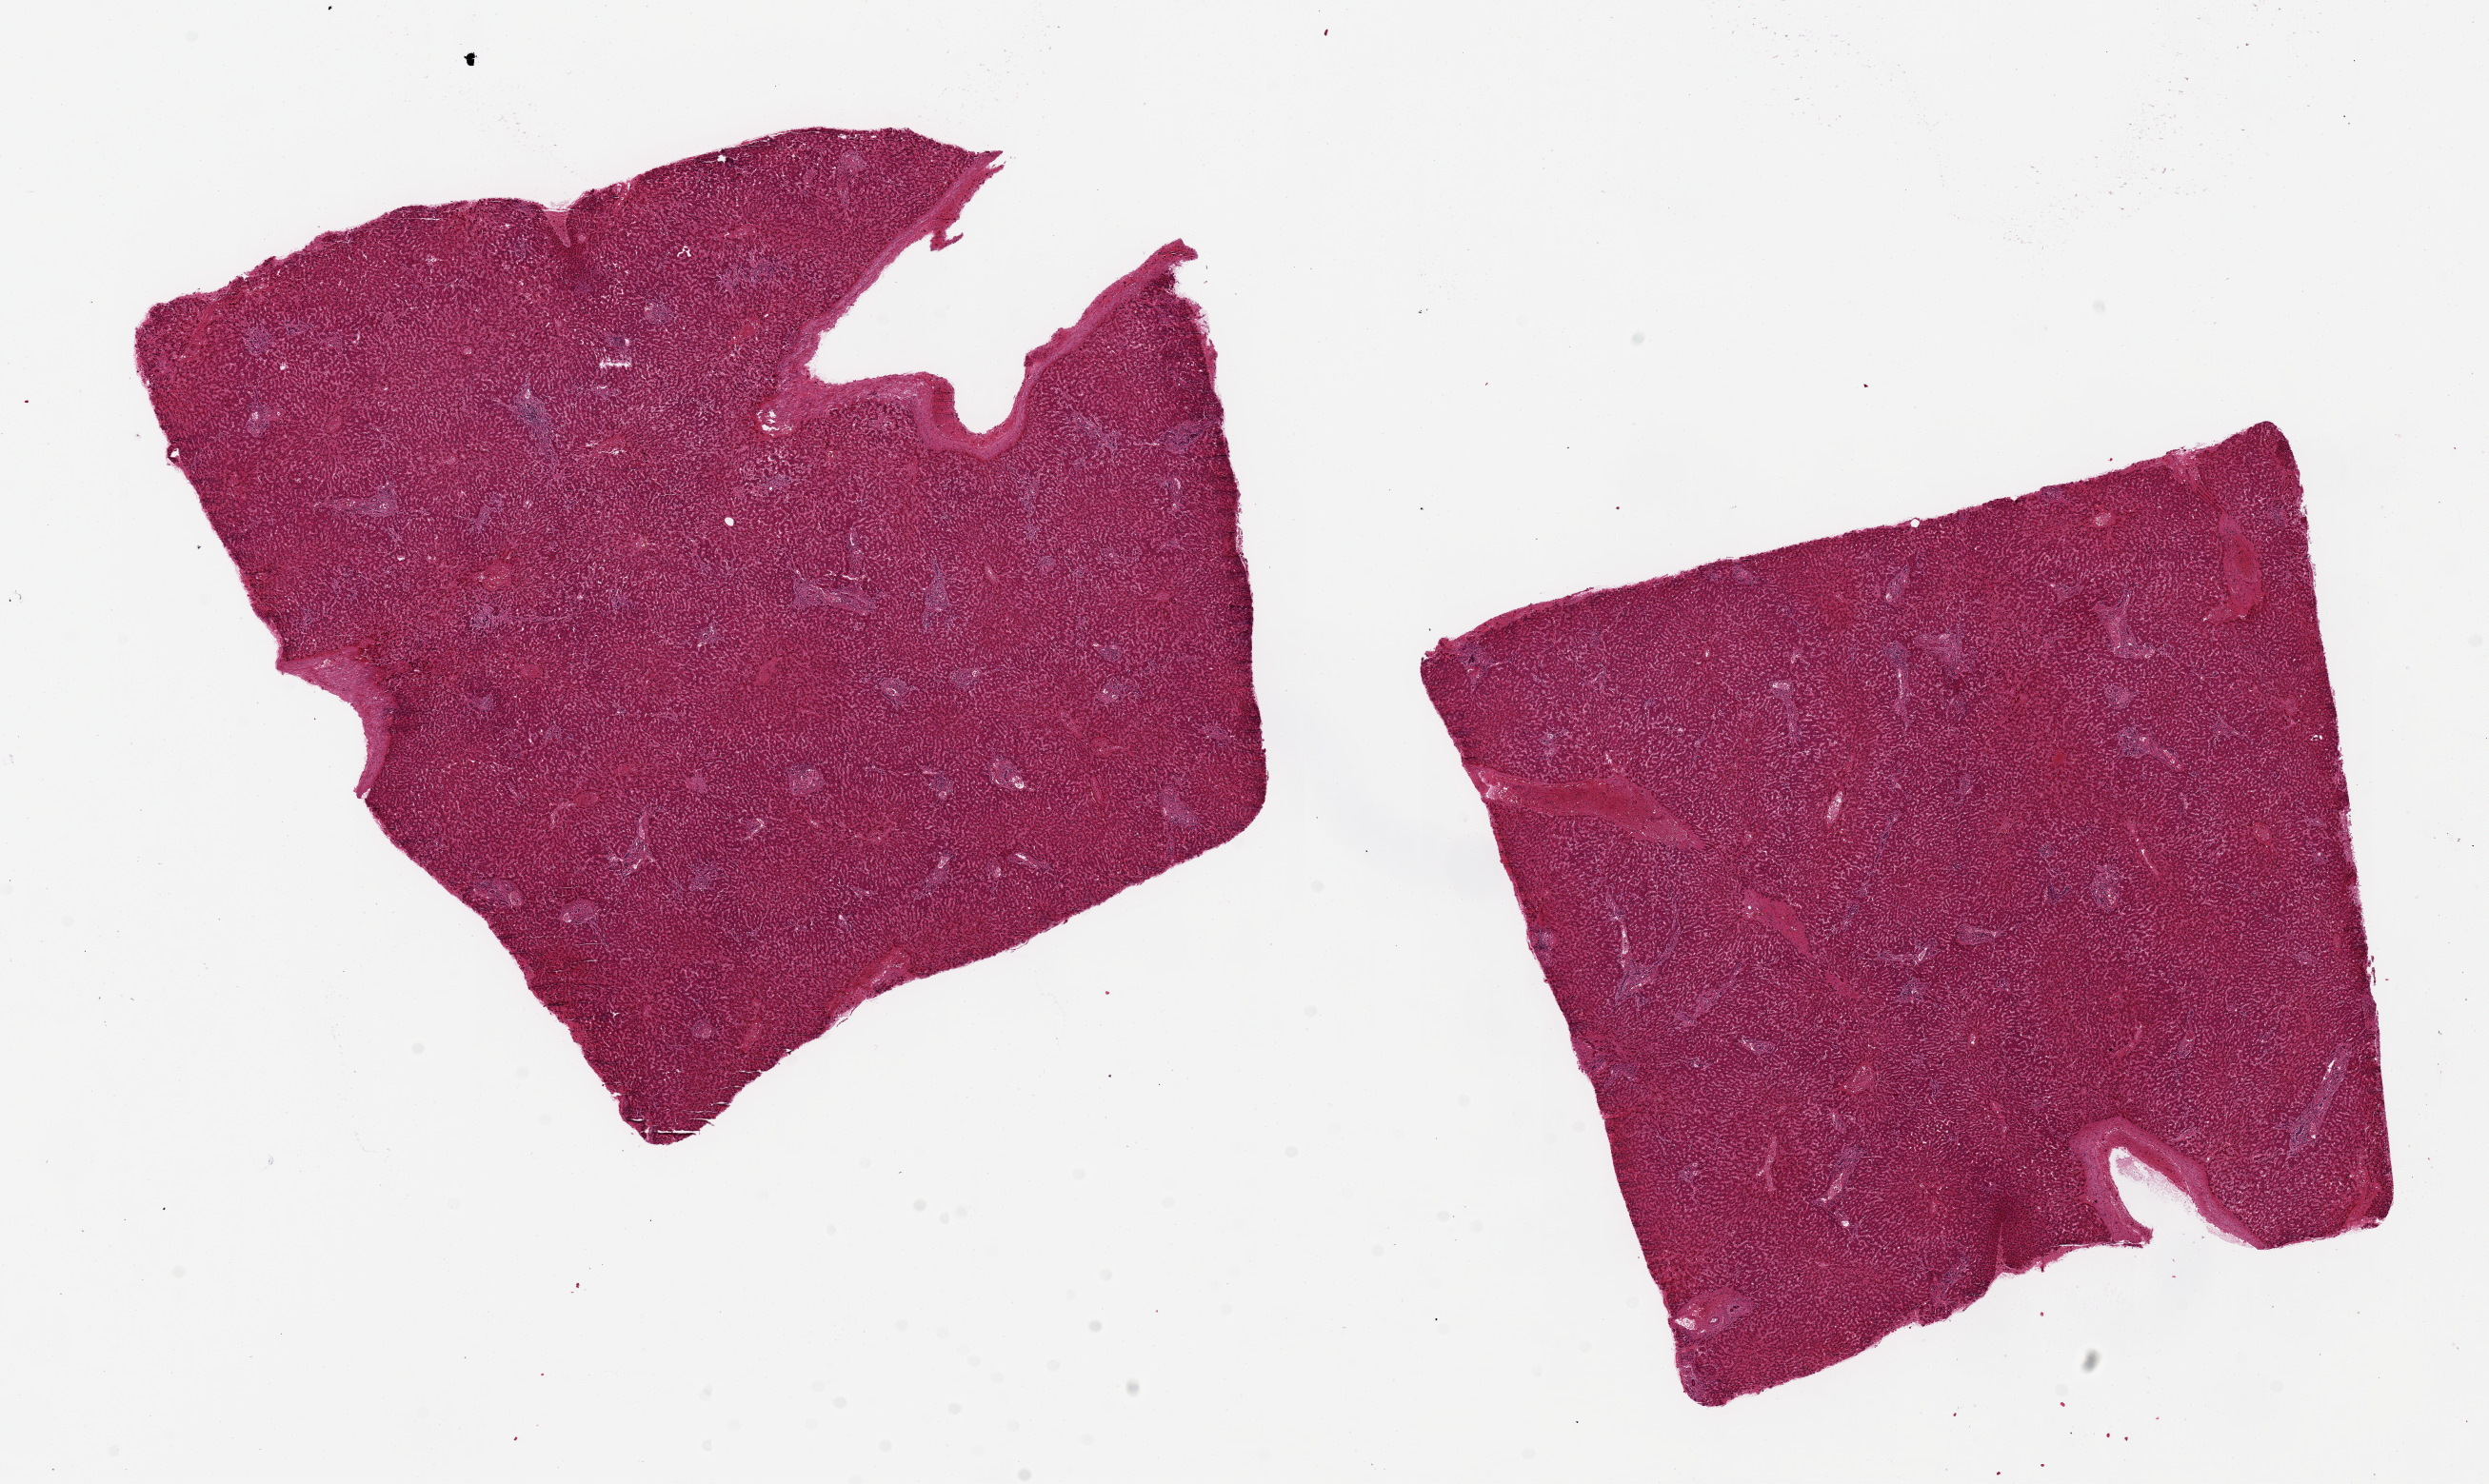
Whole-slide image, hematoxylin and eosin (H&E) stain — a low-resolution overview of the entire scanned area, about 20.7 x 12.3 mm, PAXgene-fixed, paraffin-embedded tissue, sampled site (target tissue): liver, tissue donor sample. Donor: male.
Review note (as recorded): 2 pieces, 8x8 & 7x7mm; no lesions.